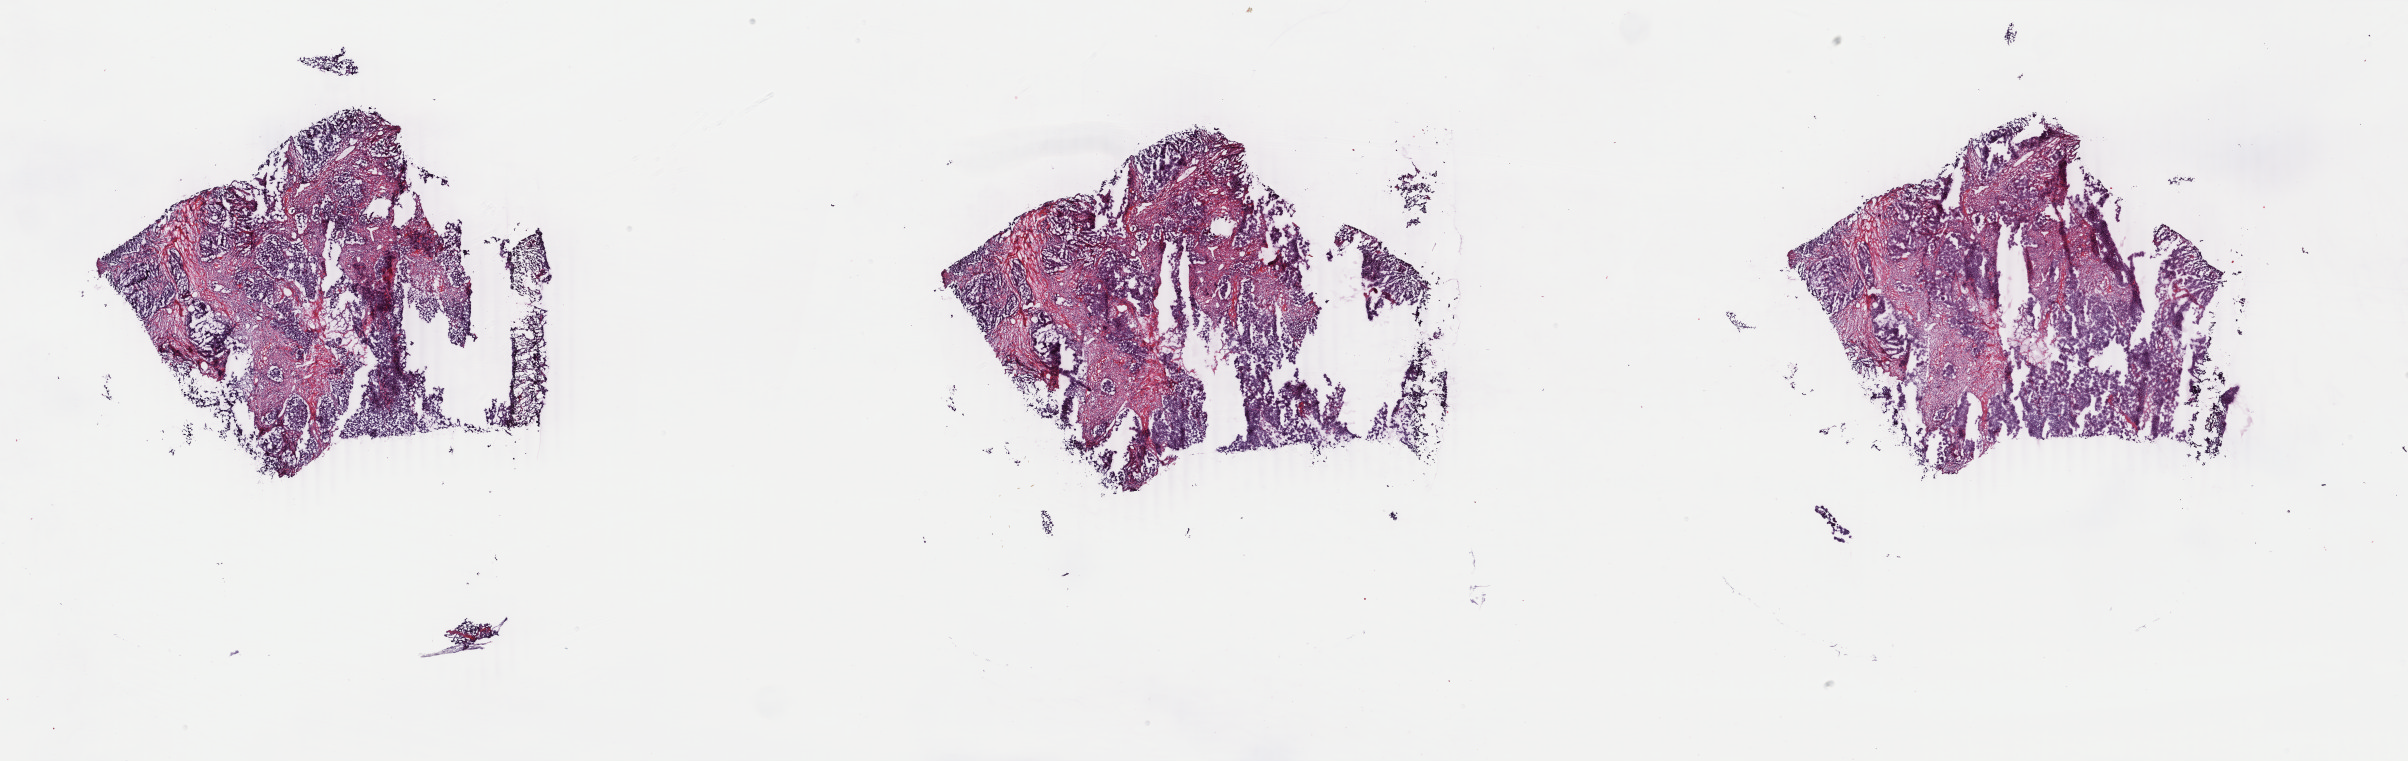
Digitized Hematoxylin and eosin (H&E) stained tissue section (whole slide), a low-resolution overview of the entire scanned area, about 38.3 x 12.1 mm (acquisition: 40x scan); frozen section; primary tumour sample from the breast. Female, age 40 years at initial diagnosis. Slide review estimates, as recorded: tumour cells 80%, tumour nuclei 80%, normal cells 0%, stromal cells 20%, necrosis 0%. Infiltration values recorded for this section: lymphocyte infiltration 2%, monocyte infiltration 0%, neutrophil infiltration 0%.
AJCC pathologic stage: IIIA (4th edition). Lymph nodes positive (case pathology): 1 of 26 examined. Laterality: left. Diagnosis: Infiltrating duct carcinoma, NOS.